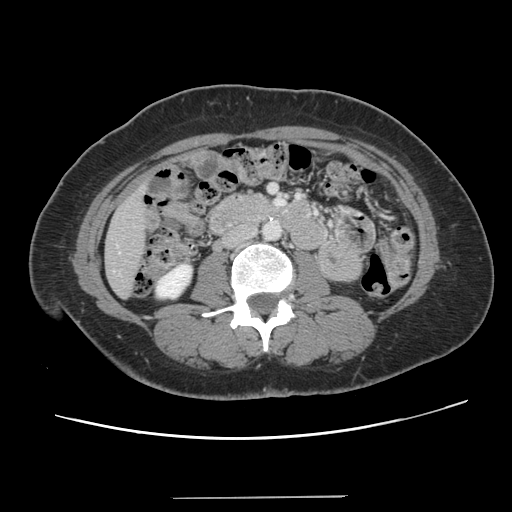
Contrast-enhanced abdominal CT, one axial slice. Position 31 of 141 along the scan axis. 120 kVp. Intravenous contrast given. Soft-tissue window (W 400 / L 40 HU). 512 × 512 image matrix, field of view 366 × 366 mm. Female patient, age 53 years. From the clinical record (not read from this slice): diagnosis: colorectal cancer liver metastases, imaged before liver resection; multiple liver metastases: no; largest metastasis: 14.5 cm; chemotherapy before resection: yes.
Structures marked on this image (outlined manually by an expert reader):
- liver: box from (x=106, y=191) to (x=146, y=297) px
- planned liver remnant (the part of the liver to remain after resection): (x=106, y=207)–(x=146, y=296)